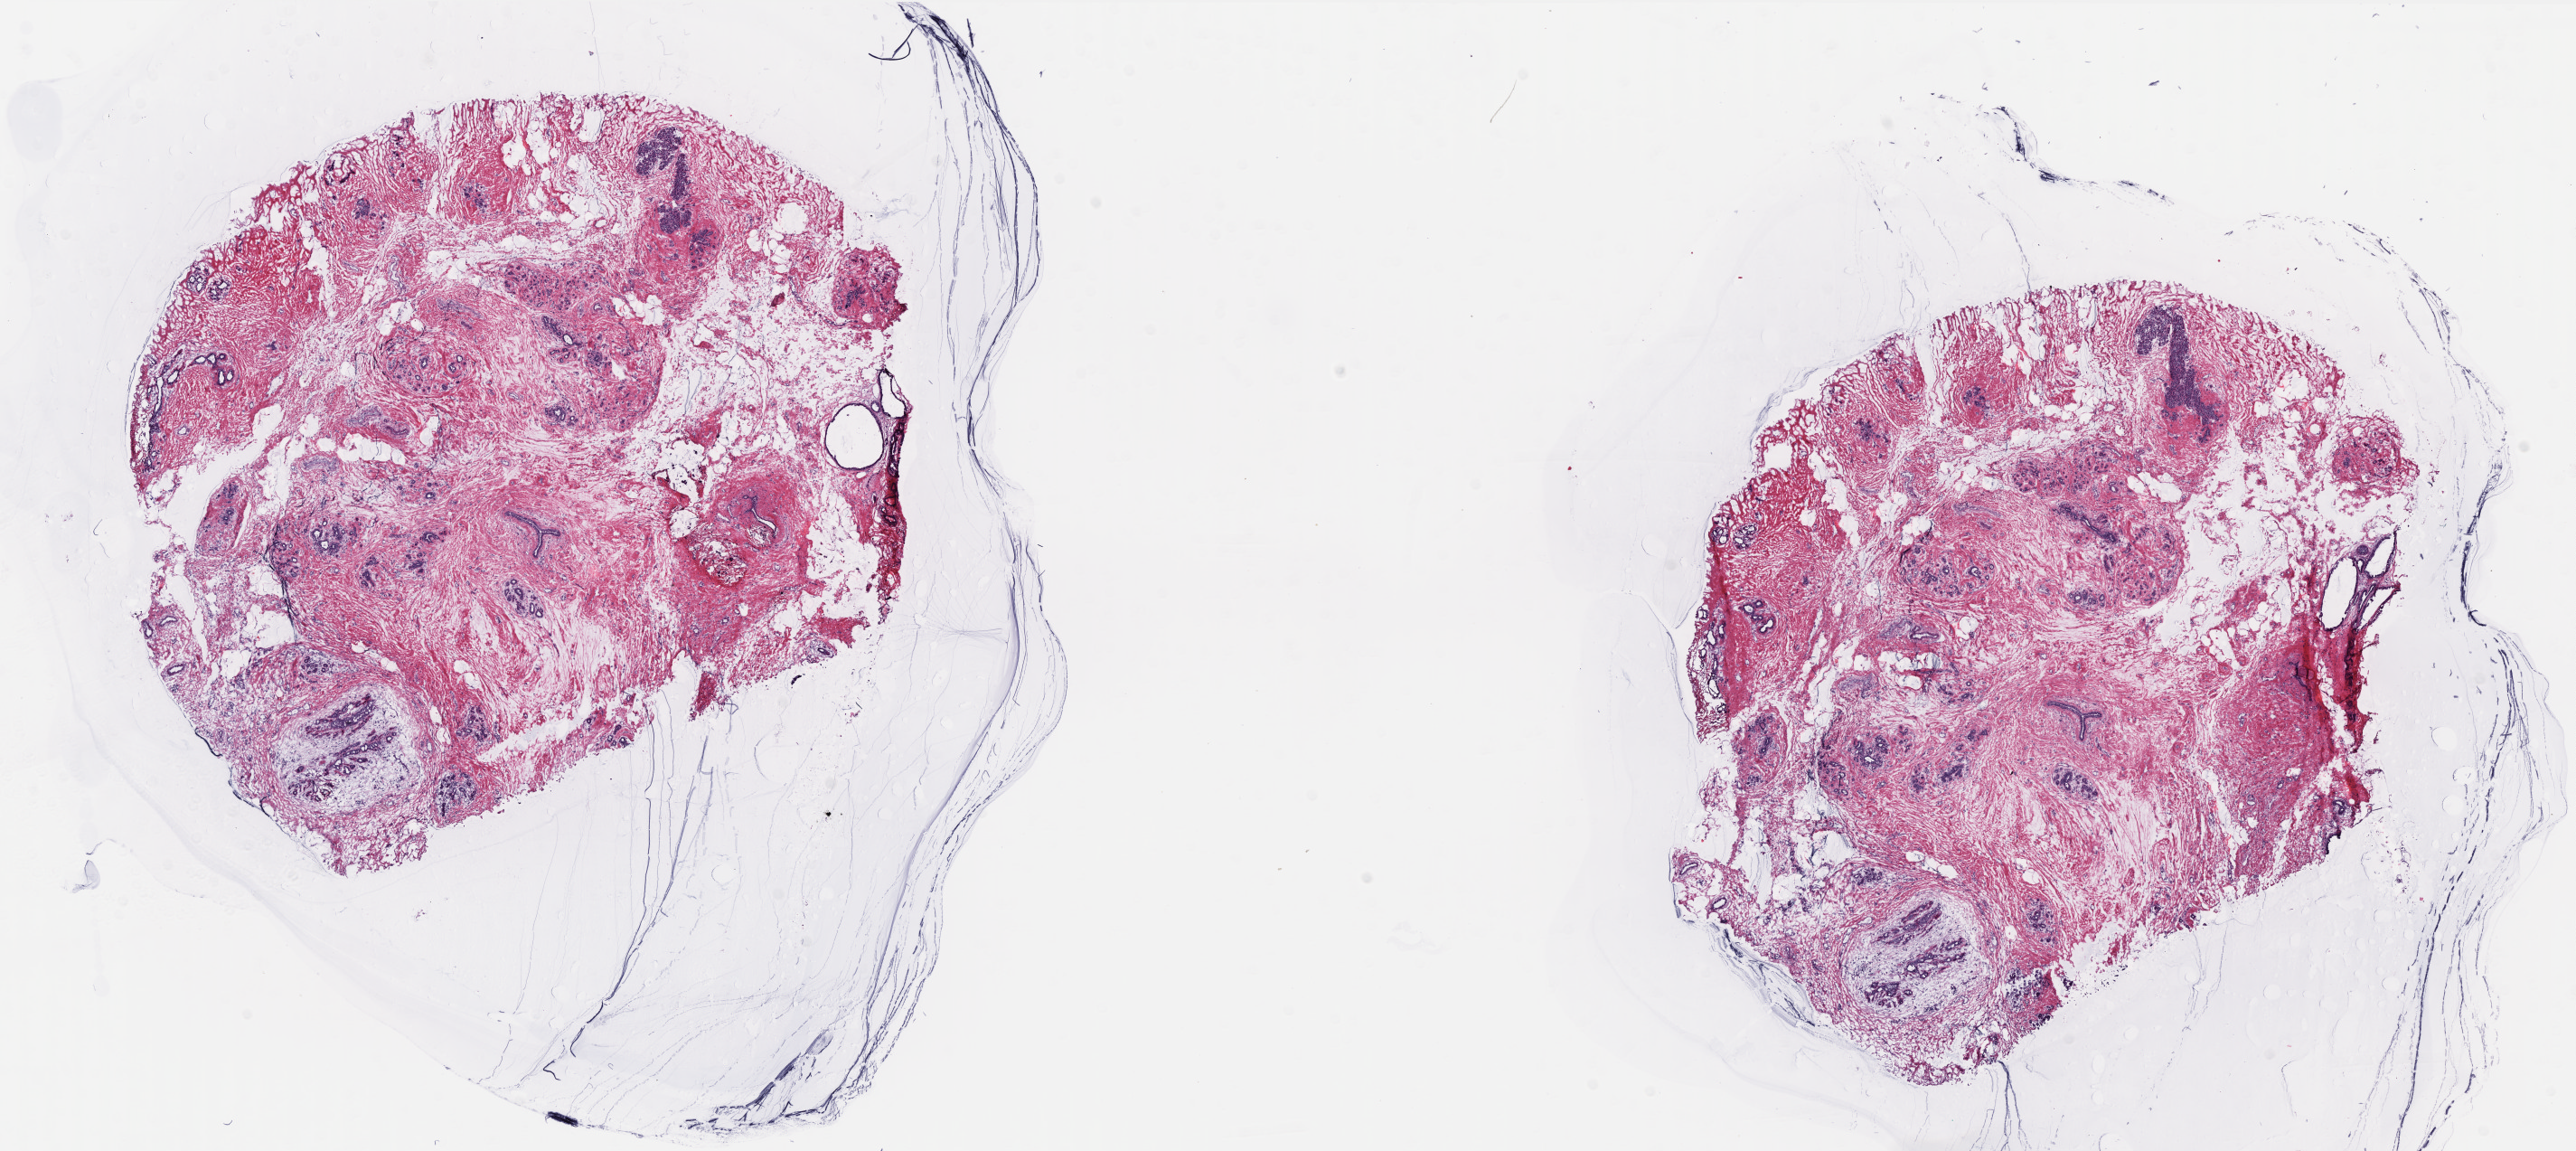
Digitized Hematoxylin and eosin (H&E) stained tissue section (whole slide) — shown as a low-resolution overview of the whole scanned area (about 22.8 x 10.2 mm, acquisition: 40x scan). Frozen section. Solid tissue normal (non-tumour tissue) sample from the breast. Female, age 57 years at initial diagnosis. Pathologist review of this section (percent, as recorded): tumour cells 0%, normal cells 100%. Inflammatory infiltration, as recorded: lymphocyte infiltration 3%, monocyte infiltration 0%, neutrophil infiltration 0%.
This section: solid tissue normal sample (biorepository sample class). Patient diagnosis: Infiltrating duct carcinoma, NOS.